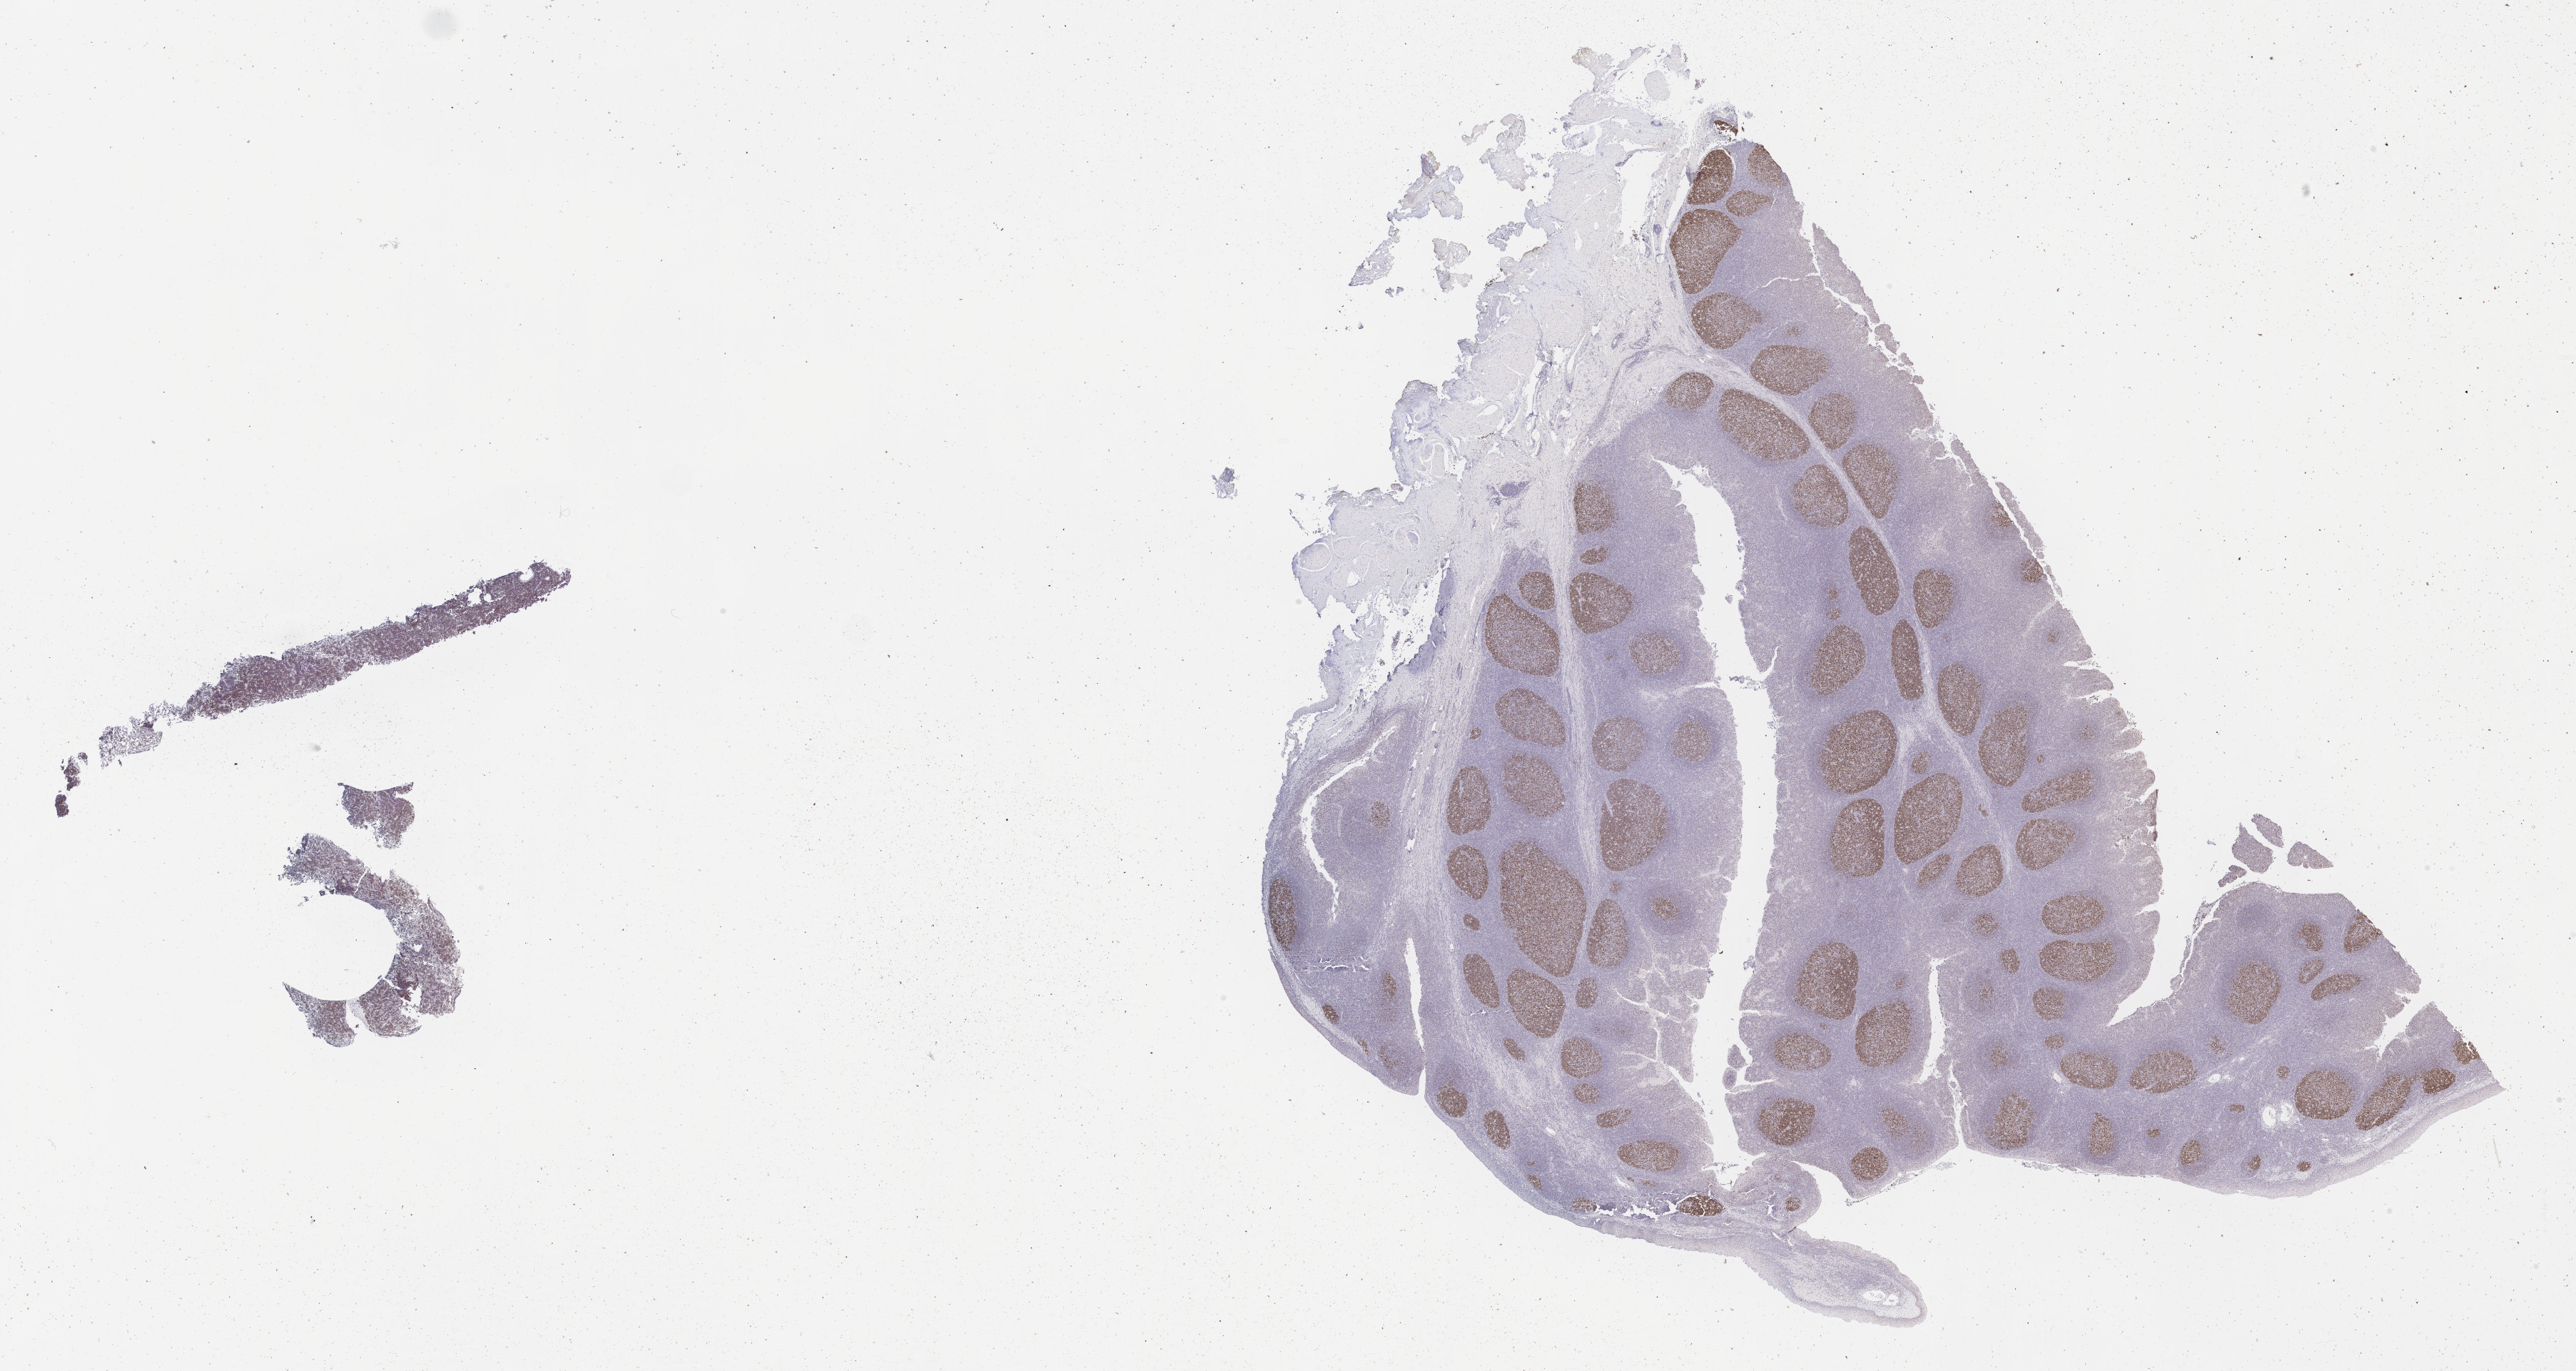
Whole-slide image, immunohistochemical stain for BCL6, low-resolution overview of the scanned area, about 29.2 x 15.5 mm. Specimen: tumor tissue. Anatomic site: ovary. Patient: female, 10 years old.
Diagnosis: Burkitt lymphoma, NOS.